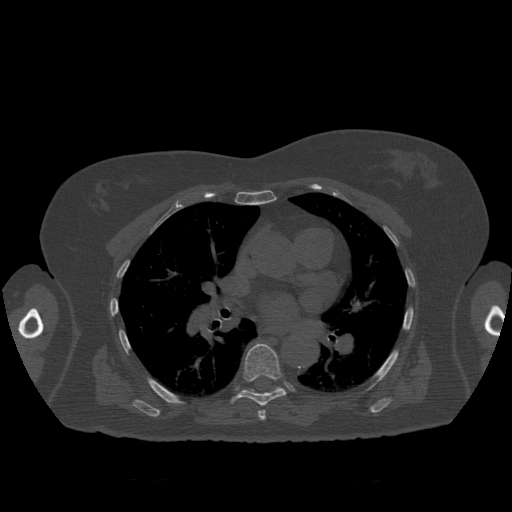
CT including the spine, one axial slice; position 395 of 399 along the scan axis; 120 kVp; bone window (W 1800 / L 400 HU); 512 × 512 image matrix. Patient age 81 years. Case-level facts recorded for this patient, not image findings: primary cancer: renal; vertebrae with lytic lesions (as recorded): L1.
Structures marked on this image (semi-automatically segmented with operator editing):
- T7 vertebra: bounding box <231,344,287,421> (left, top, right, bottom; pixels)
- T8 vertebra: <246,387,281,393>